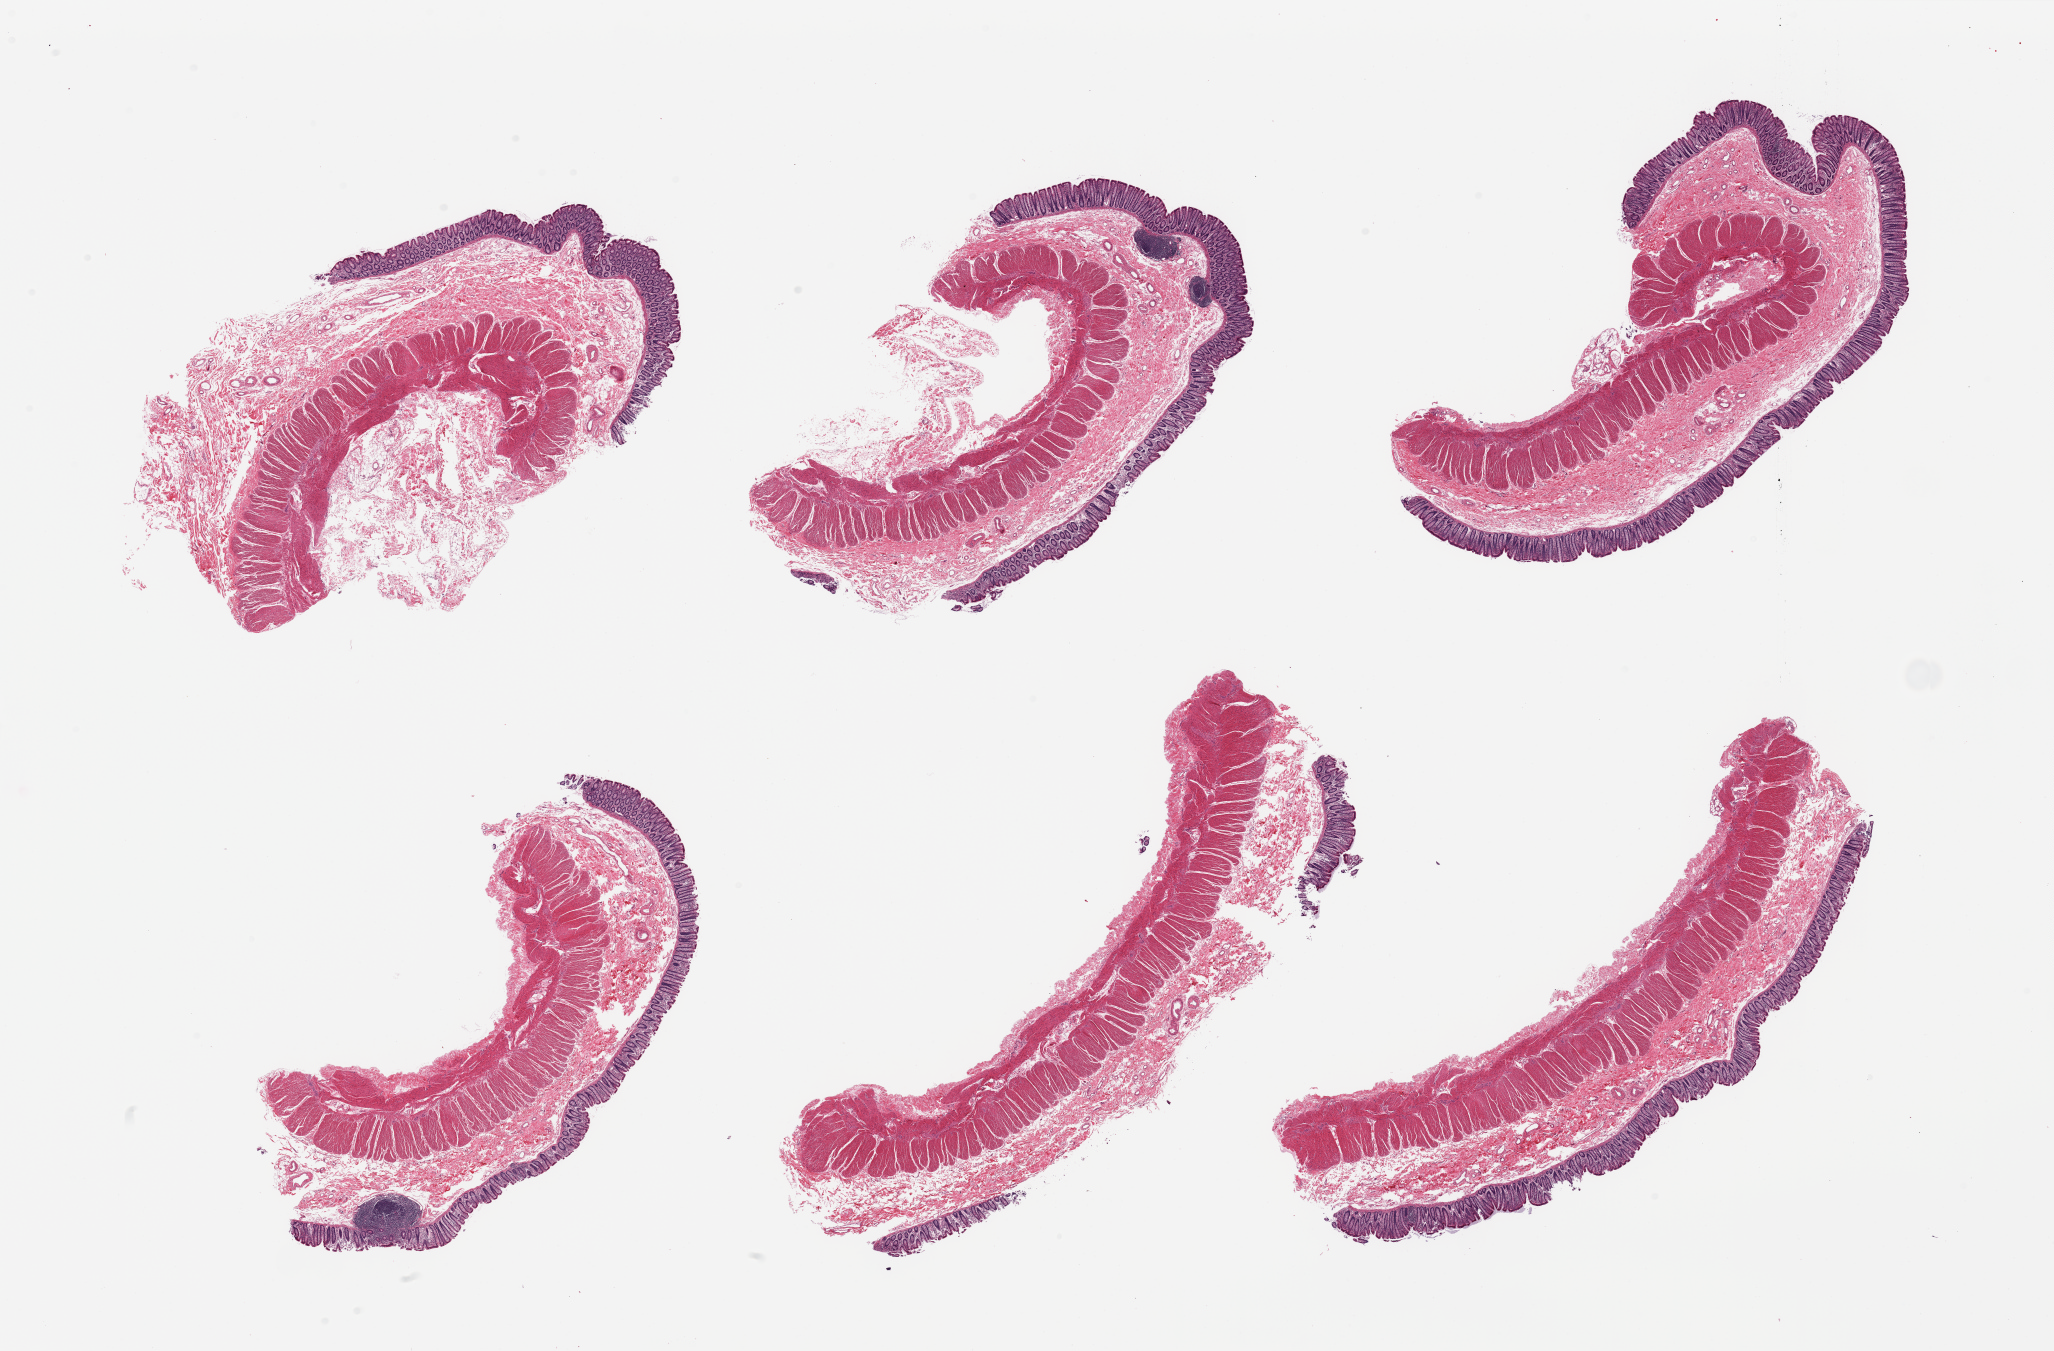
Whole-slide image, hematoxylin and eosin (H&E) stain — low-resolution overview of the scanned area, about 32.5 x 21.4 mm (acquisition: 20x scan), PAXgene-fixed, paraffin-embedded tissue, sampled site (target tissue): transverse colon, tissue donor sample.
• pathologist's review note for this sample: 6 pieces, mucosa well preserved, up to 0.5mm, 15-20% thickness